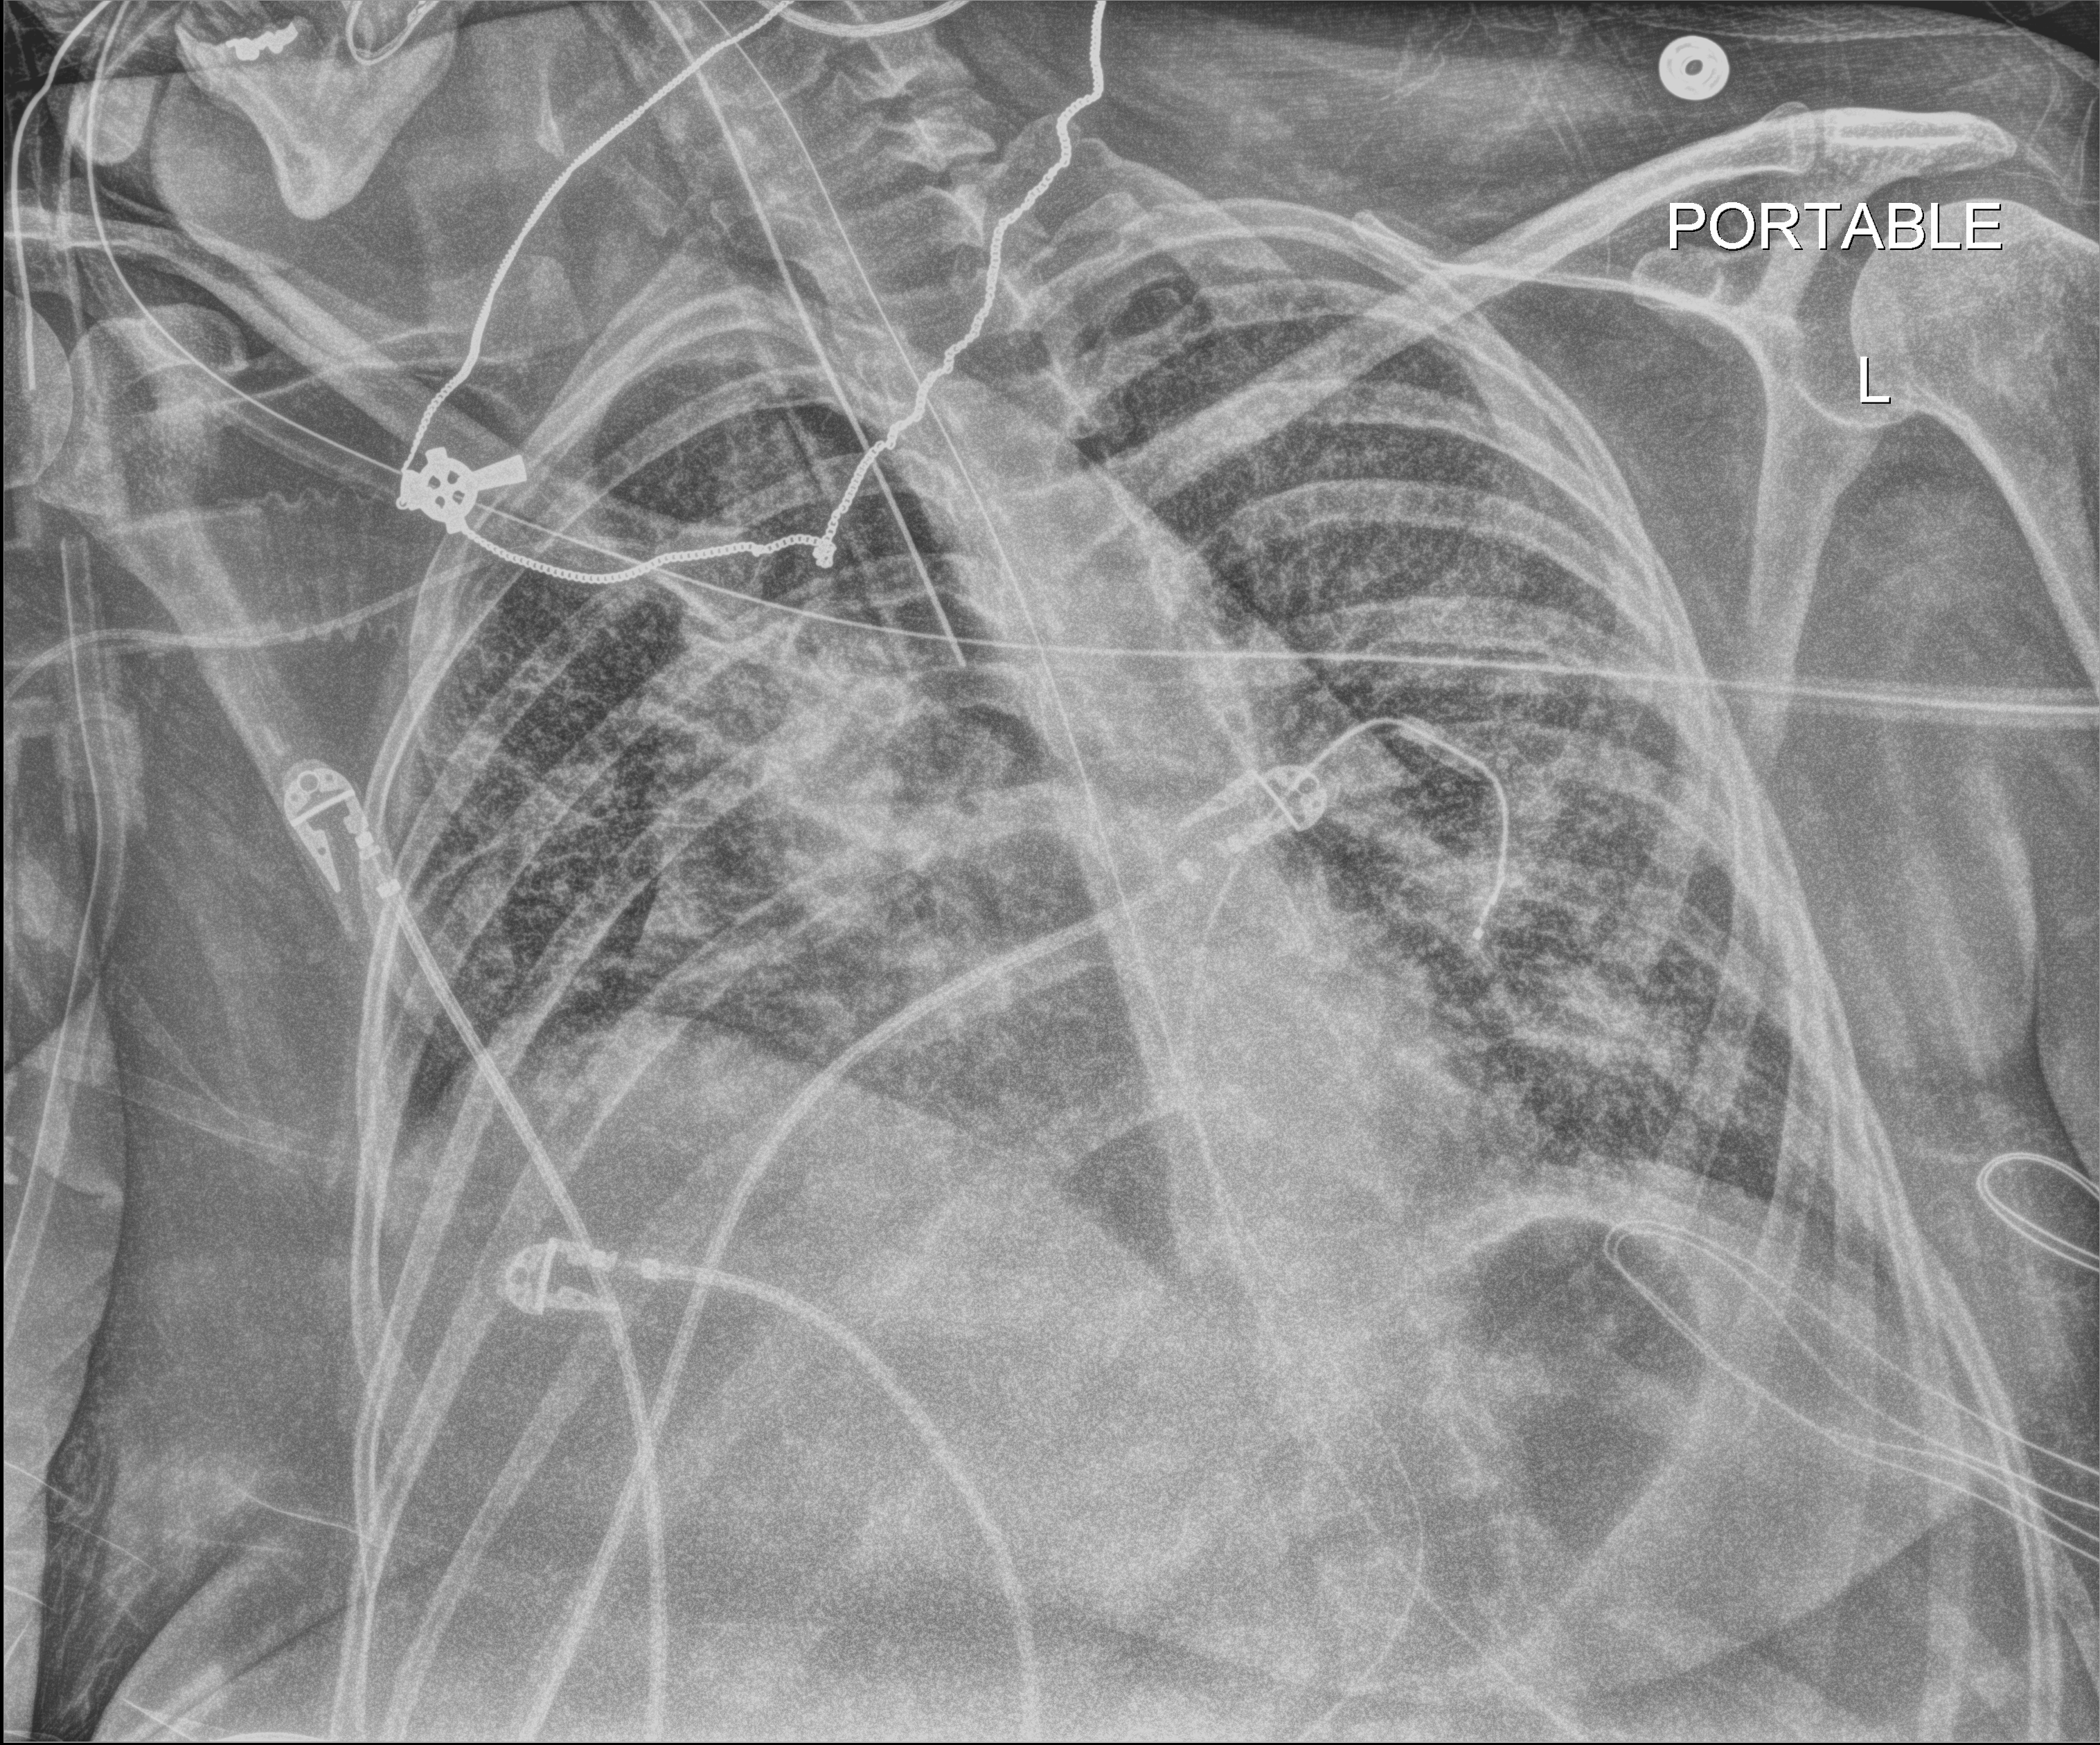
Chest X-ray, anteroposterior (AP) projection. Patient hospitalised with COVID-19; female, aged 18–59 years.
From the hospital-stay record, not from the radiograph (when in the stay this image was taken is not recorded):
- smoking status (admission record): former
- admitted to intensive care during this hospital stay: yes